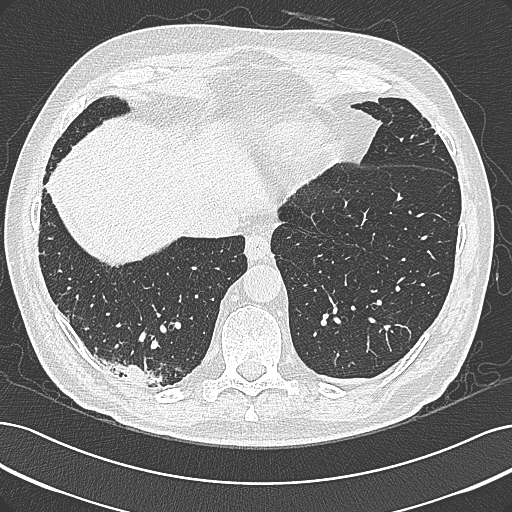
Low-dose screening chest CT, axial slice. Baseline screening round. Lung window (W 1500 / L -600 HU). 1 mm slice thickness. Slice 228 of 355 in the series. 512 × 512 image matrix, field of view 362 × 362 mm. Male, age 68 years at enrolment. Former smoker at enrolment.
- Expert reader's lesion annotation, bounding box <98,341,184,402> (left, top, right, bottom; pixels).
- No non-calcified nodule or mass ≥4 mm was recorded by the screening reader at this exam.
- Later outcome: lung cancer diagnosed 154 days after this screen — mucinous adenocarcinoma, right lower lobe, well differentiated (G1), stage IB (AJCC 6th edition), 50 mm at pathology.